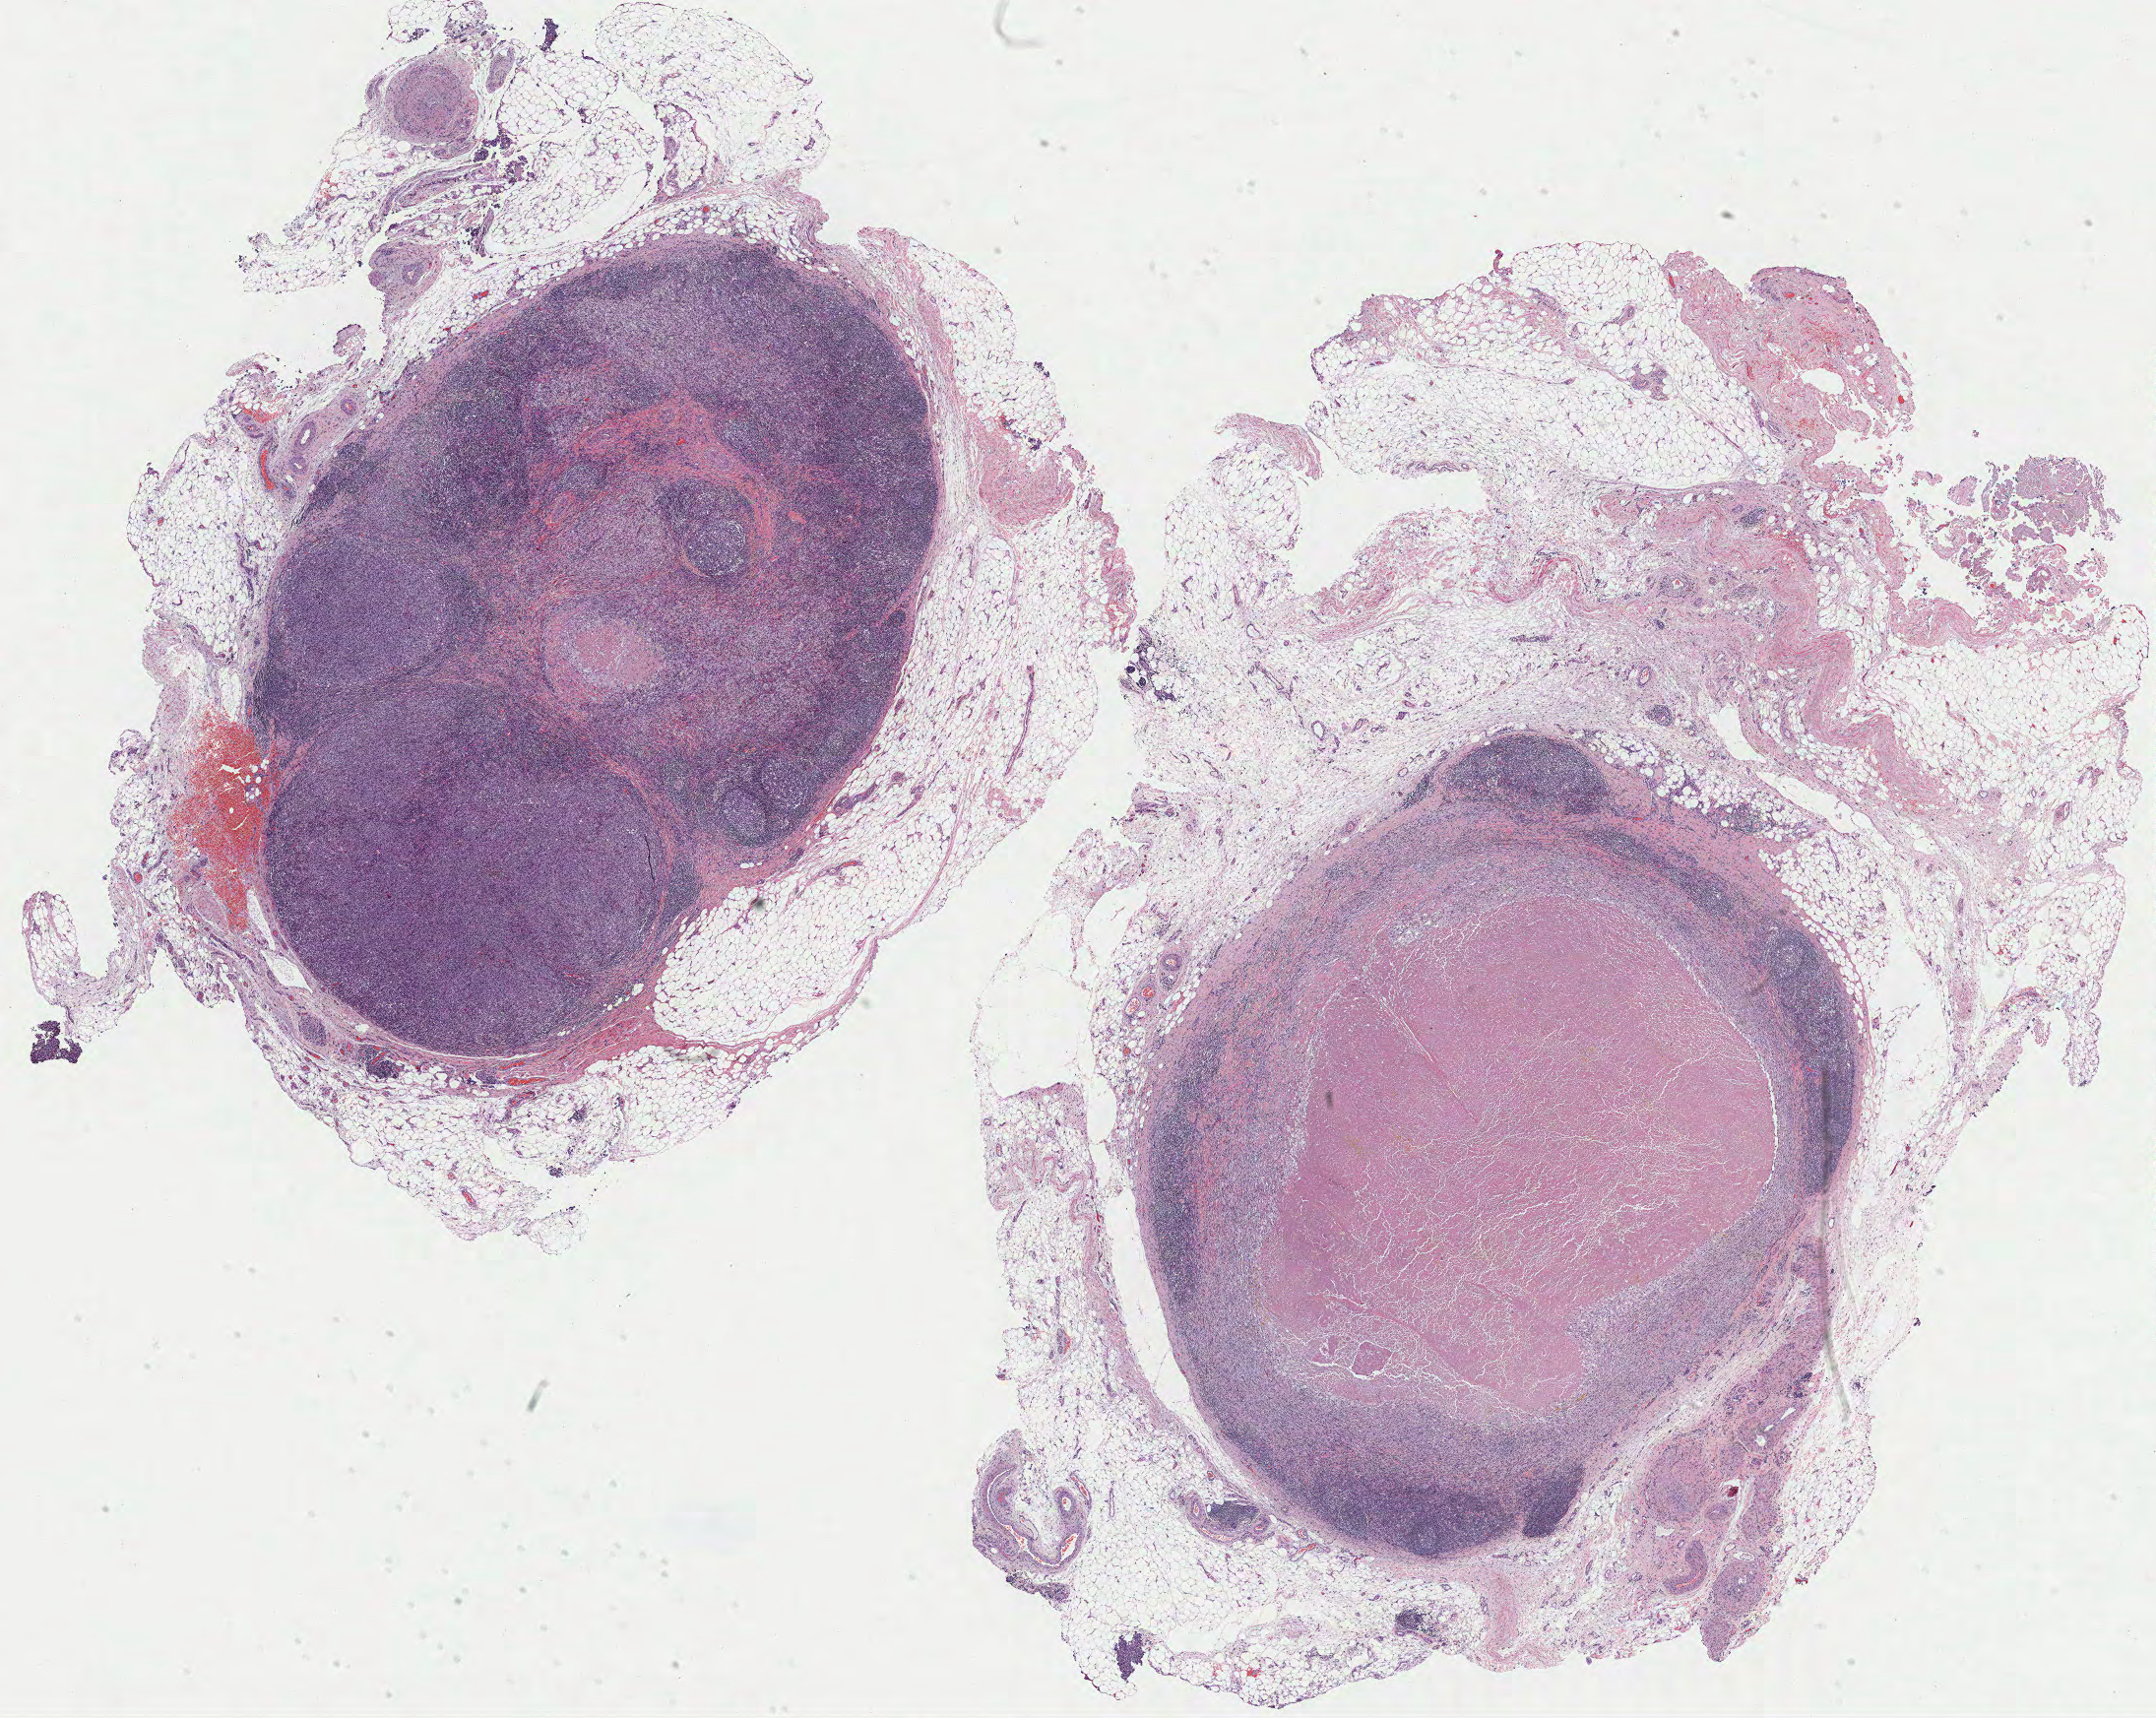
Whole-slide histology image, Hematoxylin and eosin (H&E) stained, whole scanned area (about 17.6 x 14.0 mm, slide scanned at 40x) shown as a low-resolution overview. Formalin-fixed paraffin-embedded (FFPE) diagnostic section. Metastatic tumour sample. Female, age 63 years at initial diagnosis.
This section: metastatic tumour tissue. Patient diagnosis: Malignant melanoma, NOS.